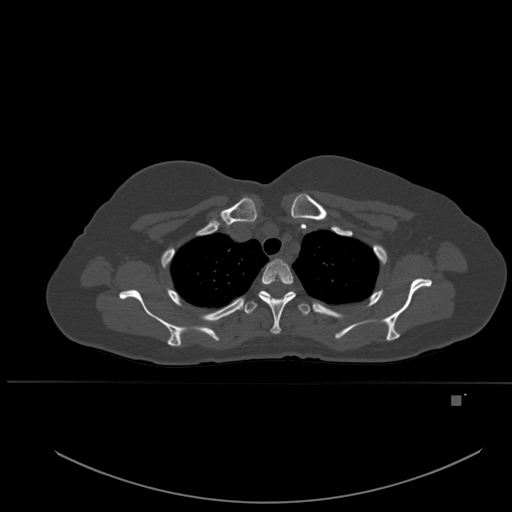
CT including the spine, one axial slice. Bone window (W 1800 / L 400 HU). 512 × 512 image matrix, field of view 443 × 443 mm. Patient: female, 49 years. From the clinical record (not read from this slice): primary cancer: breast; vertebrae with lytic lesions (as recorded): L3, T12, L4.
Outlined on this slice (semi-automatic segmentation, software-assisted and operator-edited):
- T2 vertebra: bounding box [x1, y1, x2, y2] px = [259, 259, 296, 334]
- T3 vertebra: [244, 290, 311, 315]